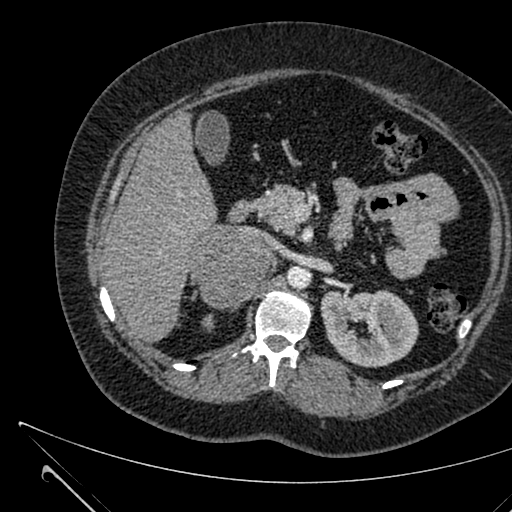
Contrast-enhanced abdominal CT, one axial slice; slice 394 of 731 in the series (ordered by position); soft-tissue window (W 400 / L 40 HU); 1 mm slice thickness; 512 × 512 image matrix, field of view 376 × 376 mm. Patient: female, 36 years. Case-level facts recorded for this patient, not image findings: diagnosis: adrenocortical carcinoma; tumour side: right adrenal; tumour size at pathology: 10 cm; Ki-67 index: 20 %; stage (as recorded): 4.
Annotated regions visible in this slice (semi-automatic segmentation, software-assisted and operator-edited):
- mass: bounding box (x1, y1, x2, y2) in pixels: (190, 226, 268, 305)